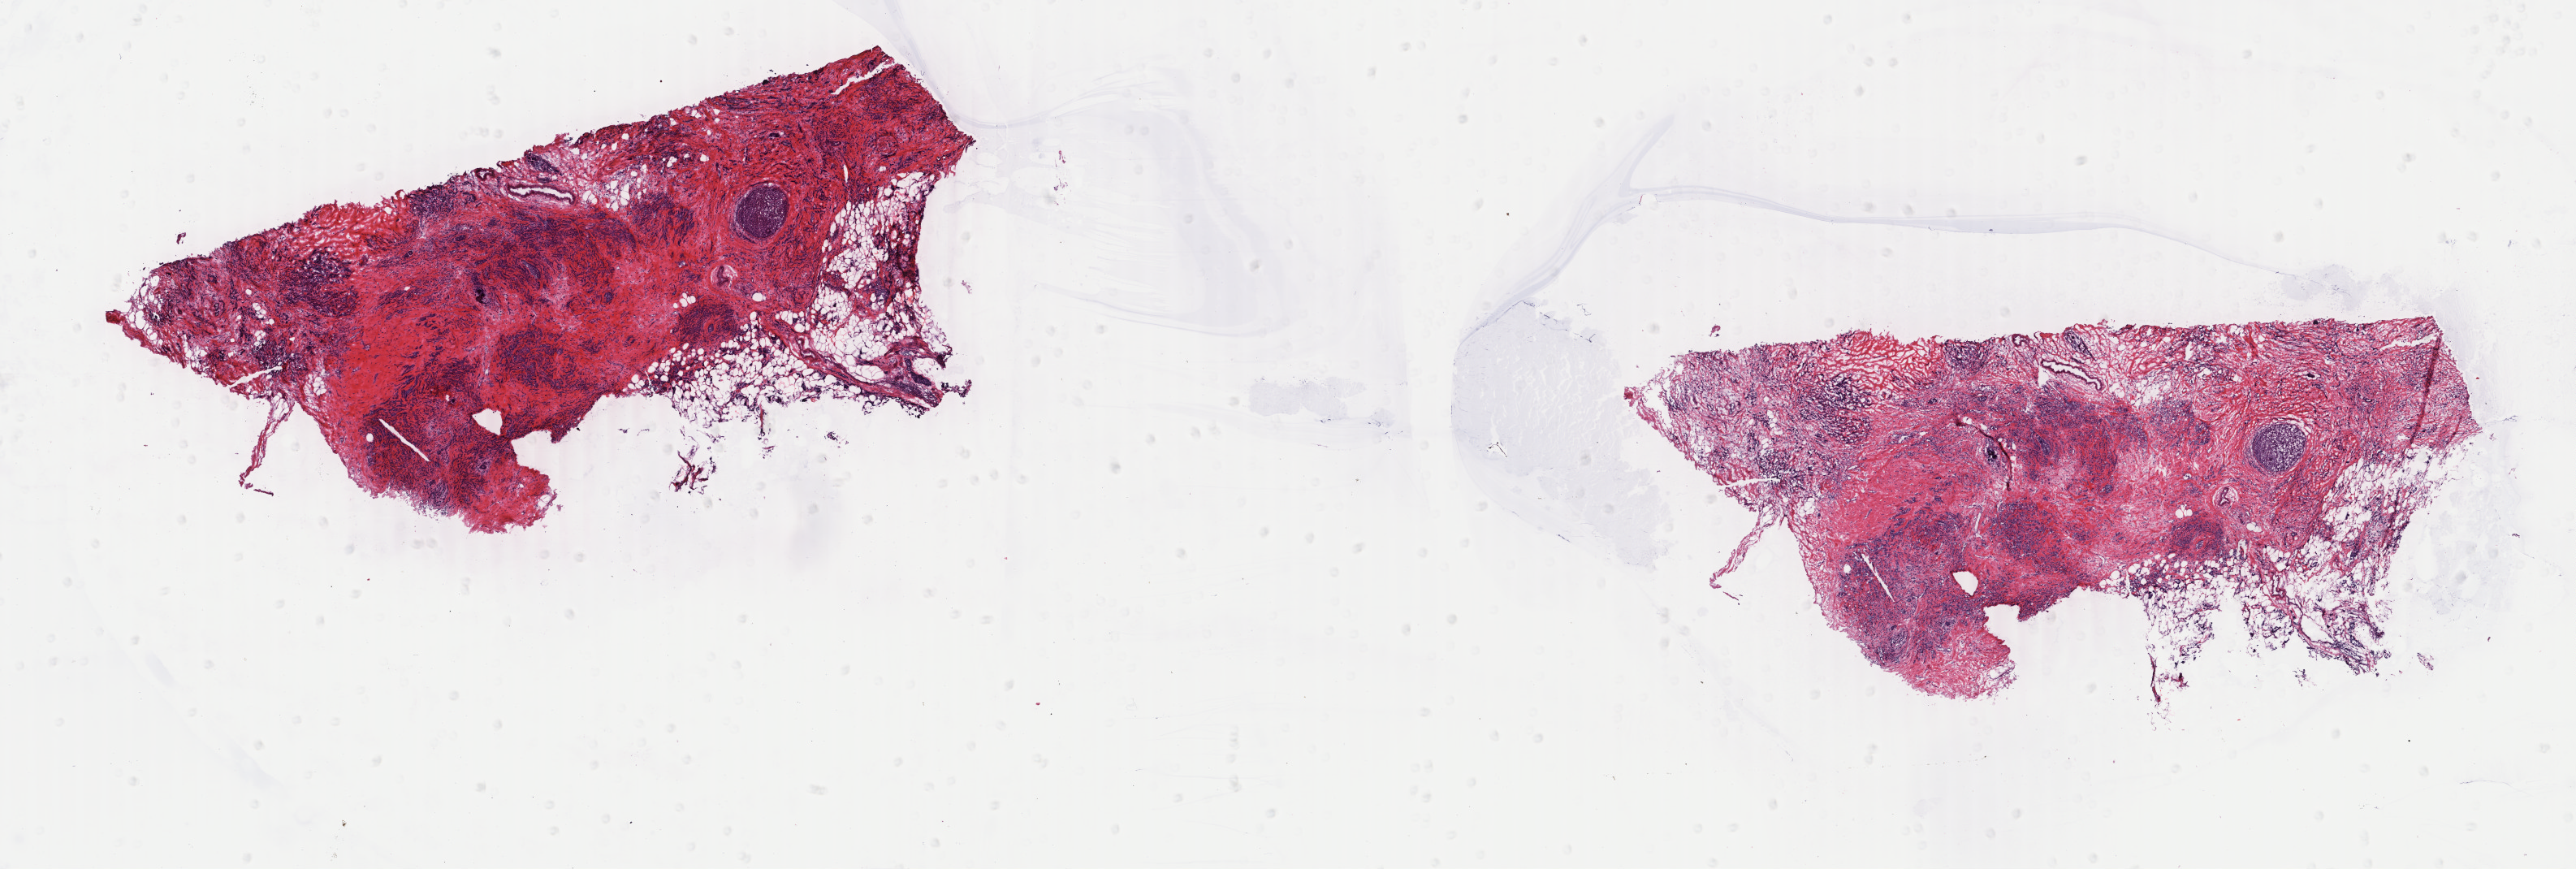
Hematoxylin and eosin (H&E) stained whole-slide image — whole scanned area (about 25.2 x 8.5 mm) shown as a low-resolution overview. Frozen section from the top of the tissue portion. Primary tumour sample from the breast. Female, age 60 years at initial diagnosis.
Pathologic diagnosis: Lobular carcinoma, NOS.